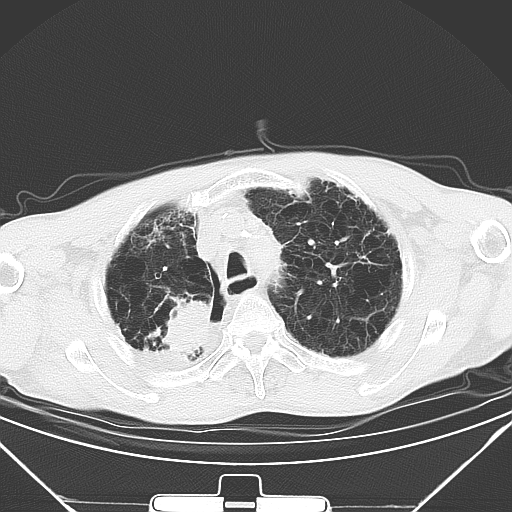
Chest CT, one axial slice; slice 39 of 50 in the series (ordered by position); lung window (W 1500 / L -600 HU); 512 × 512 image matrix. Patient: male, 65 years. Case-level facts recorded for this patient, not image findings: clinical TNM (as recorded): T3 N1 M1a.
Outlined on this slice (bounding box drawn by a radiologist):
- lung tumour (recorded histology: squamous cell carcinoma): bounding box <165,293,216,358> (left, top, right, bottom; pixels)